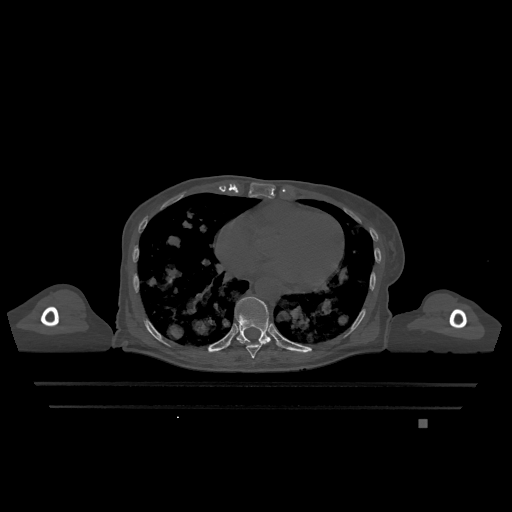
CT including the spine, one axial slice. Position 667 of 1317 along the scan axis. Bone window (W 1800 / L 400 HU). 0.5 mm slice thickness. 512 × 512 image matrix, field of view 500 × 500 mm. Patient: female, 74 years. Case-level facts recorded for this patient, not image findings: primary cancer: lung.
Structures marked on this image (semi-automatically segmented with operator editing):
- T10 vertebra: bounding box <235,297,271,342> (left, top, right, bottom; pixels)
- T9 vertebra: <238,340,271,359>